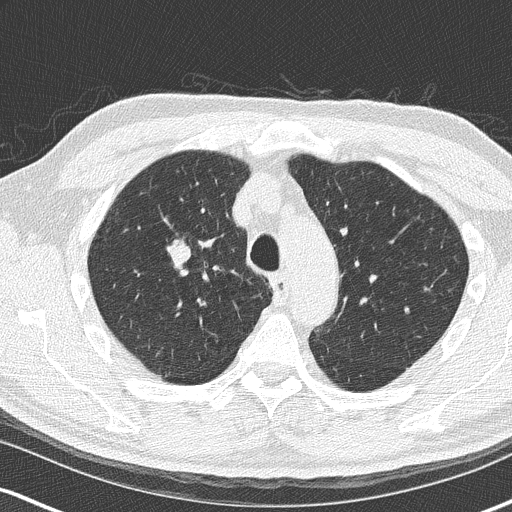
Low-dose screening chest CT, axial slice, second annual screen, lung window (W 1500 / L -600 HU), 512 × 512 image matrix, field of view 320 × 320 mm. Male, age 68 years at enrolment. Current smoker at enrolment.
- Lesion marked by an expert reader, box from (x=152, y=229) to (x=216, y=291) px.
- Screening reader's record for this exam (one nodule recorded; not confirmed to be the boxed lesion): non-calcified nodule or mass ≥4 mm, right upper lobe, 18 × 15 mm, smooth margins, soft tissue attenuation, pre-existing on the prior screen: no.
- Official screen result: positive, change unspecified: nodule(s) >= 4 mm or enlarging nodule(s), mass(es), or other non-specific abnormalities suspicious for lung cancer.
- Later outcome: lung cancer diagnosed 136 days after this screen — small cell carcinoma, NOS, right upper lobe, stage IIIB (AJCC 6th edition), 20 mm at pathology.